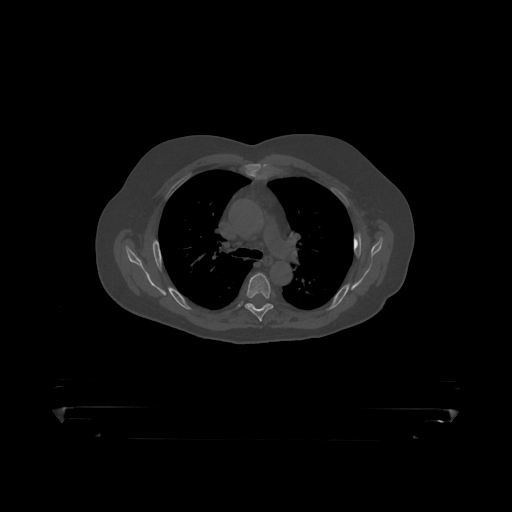
CT including the spine, one axial slice; position 318 of 390 along the scan axis; reconstruction kernel STANDARD; bone window (W 1800 / L 400 HU); 512 × 512 image matrix, field of view 650 × 650 mm. Male patient, age 60 years. Case-level facts recorded for this patient, not image findings: primary cancer: prostate.
Annotated regions visible in this slice (semi-automatically segmented with operator editing):
- T5 vertebra: bounding box <245,274,274,319> (left, top, right, bottom; pixels)
- T6 vertebra: <247,303,273,308>